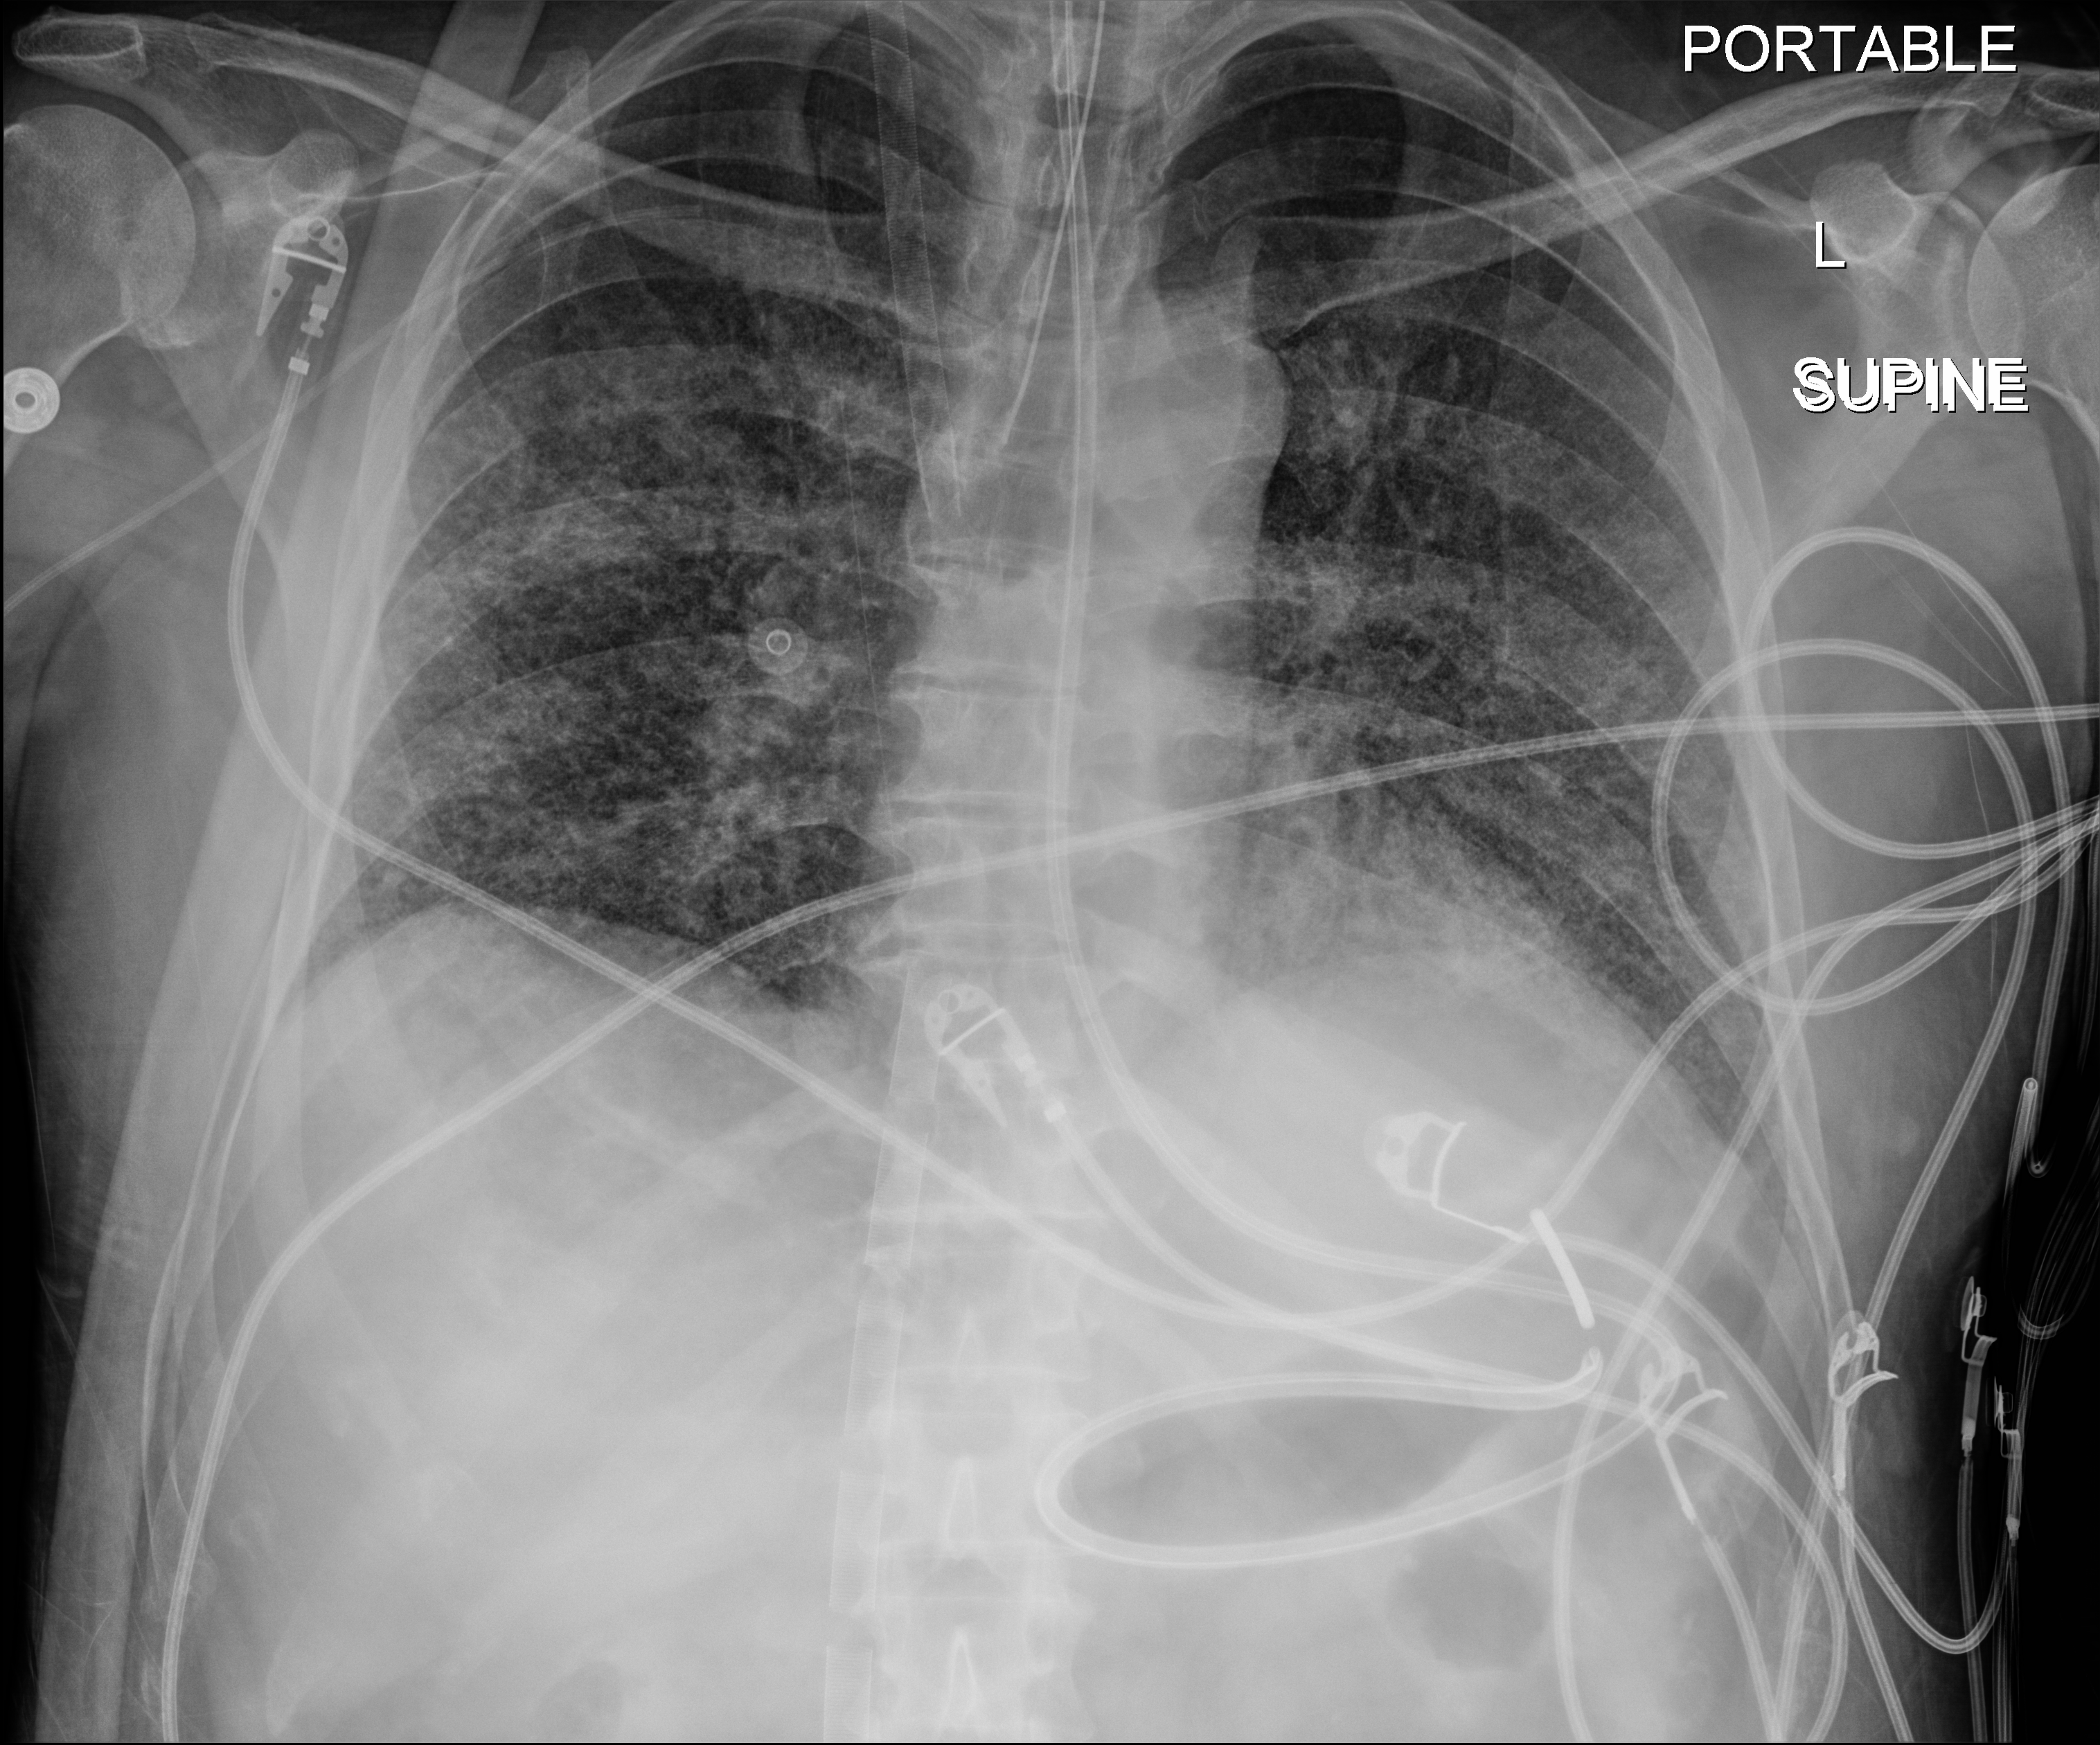
Chest X-ray (portable), anteroposterior (AP) projection. Patient hospitalised with COVID-19; male, aged 18–59 years.
Hospital-stay facts (about this admission, not read from this image; timing relative to this image not recorded):
- other chronic lung disease (admission record): no
- chronic kidney disease (admission record): no